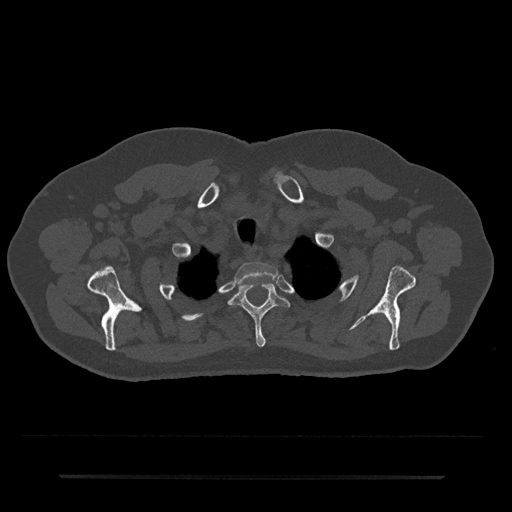
CT including the spine, one axial slice; slice 610 of 797 in the series (ordered by position); 120 kVp; bone window (W 1800 / L 400 HU); 0.5 mm slice thickness; 512 × 512 image matrix, field of view 437 × 437 mm. Patient: male, 69 years. From the clinical record (not read from this slice): primary cancer: prostate.
Annotated regions visible in this slice (semi-automatic segmentation, software-assisted and operator-edited):
- T1 vertebra: bounding box [x1, y1, x2, y2] px = [235, 262, 279, 284]
- T2 vertebra: [229, 283, 291, 347]